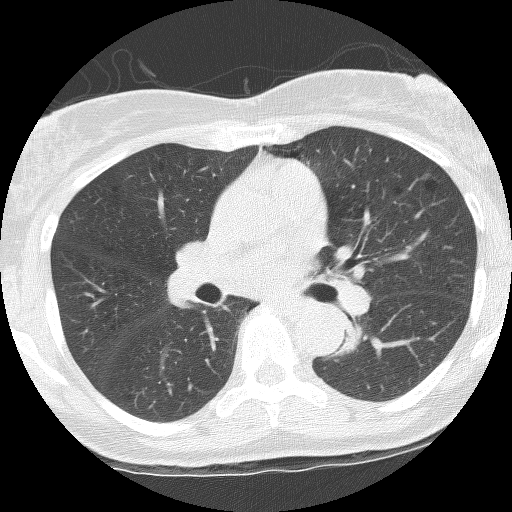
Axial slice from a low-dose chest CT screening exam; third screening round (two years after baseline); lung window (W 1500 / L -600 HU); 2.5 mm slice thickness; lung (sharp) reconstruction kernel (BONE). Female participant, aged 62 years at enrolment. Former smoker at enrolment.
Expert-annotated lung lesion, box from (x=325, y=316) to (x=380, y=360) px. The screening reader recorded 3 non-calcified nodules or masses ≥4 mm on this exam (right upper lobe, left lower lobe, left upper lobe); which of them this box marks is not recorded. Later outcome: lung cancer diagnosed 165 days after this screen — squamous cell carcinoma, NOS, left lower lobe, stage IIIB (AJCC 6th edition), 31 mm at pathology.